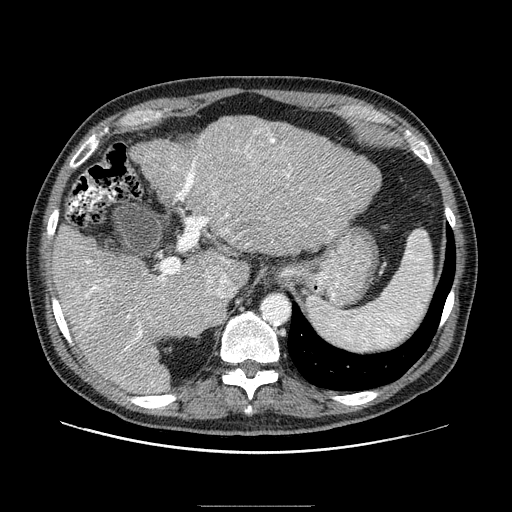
Contrast-enhanced abdominal CT (liver protocol), one axial slice; slice 59 of 99 in the series (ordered by position); reconstruction kernel STANDARD; one of 2 acquisitions stored at this slice position; soft-tissue window (W 400 / L 40 HU); 512 × 512 image matrix. Case-level facts recorded for this patient, not image findings: diagnosis: hepatocellular carcinoma (patient treated with transarterial chemoembolisation; whether this scan precedes or follows treatment is not stated here); TNM stage (as recorded): Stage-II.
Annotated regions visible in this slice (semi-automatic segmentation, software-assisted and operator-edited):
- abdominal aorta: box from (x=262, y=295) to (x=289, y=323) px
- liver parenchyma outside the tumour (the mass and vessels are separate outlines, so this box may not span the whole liver): (x=52, y=116)–(x=380, y=392)
- mass: (x=245, y=125)–(x=286, y=171)
- liver vessels: (x=76, y=160)–(x=338, y=386)